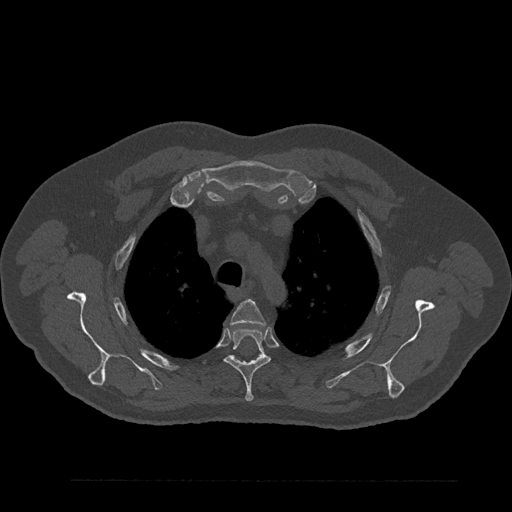
CT including the spine, one axial slice. Position 649 of 797 along the scan axis. 120 kVp. Bone window (W 1800 / L 400 HU). 512 × 512 image matrix, field of view 430 × 430 mm. Patient: male, 61 years. Case-level facts recorded for this patient, not image findings: primary cancer: prostate.
Annotated regions visible in this slice (semi-automatic segmentation, software-assisted and operator-edited):
- T3 vertebra: bounding box [x1, y1, x2, y2] px = [231, 300, 266, 325]
- T4 vertebra: [224, 328, 270, 402]
- T5 vertebra: [260, 356, 262, 358]